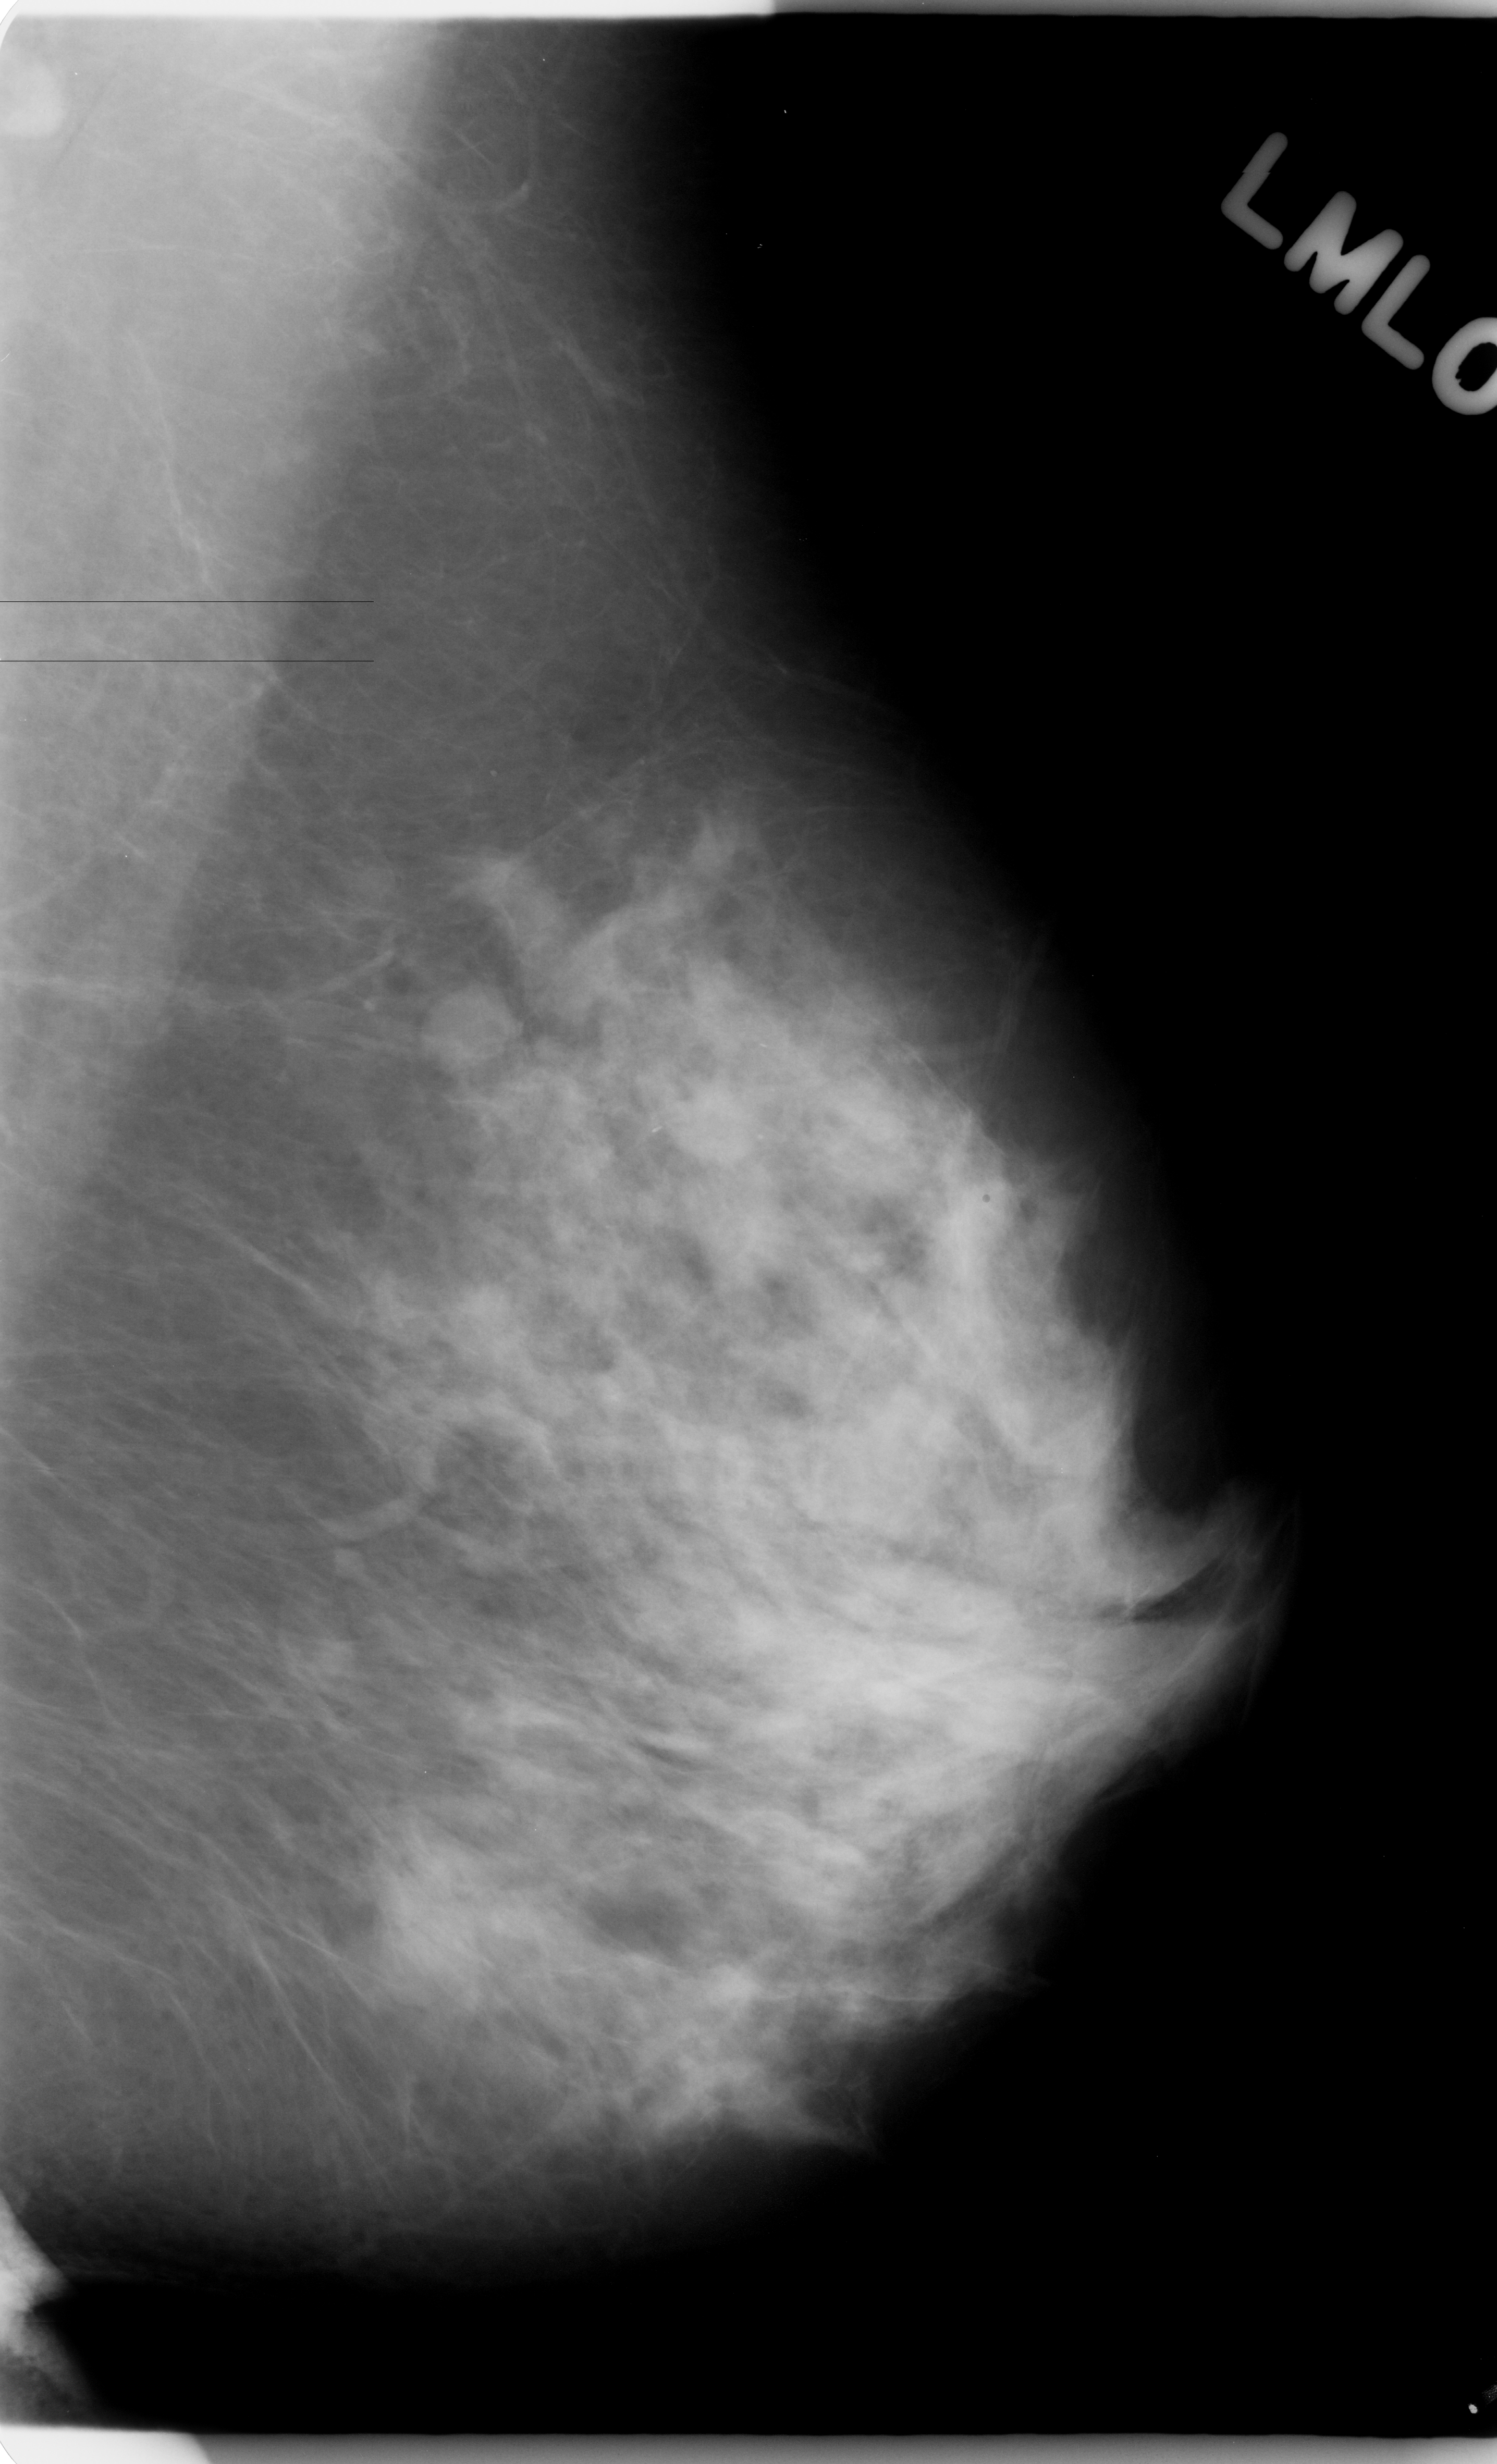
Scanned film-screen mammogram; left breast; MLO view; BI-RADS breast density category 2 (scale 1–4); 1497 × 2464 image matrix.
Marked abnormalities (boxes around the expert regions of interest):
- mass, shape oval, margins circumscribed; BI-RADS assessment category 3; subtlety rating 5 on a 1 (subtle) to 5 (obvious) scale; pathology result (as recorded, not read from the image): benign: bounding box <420,980,517,1073> (left, top, right, bottom; pixels)